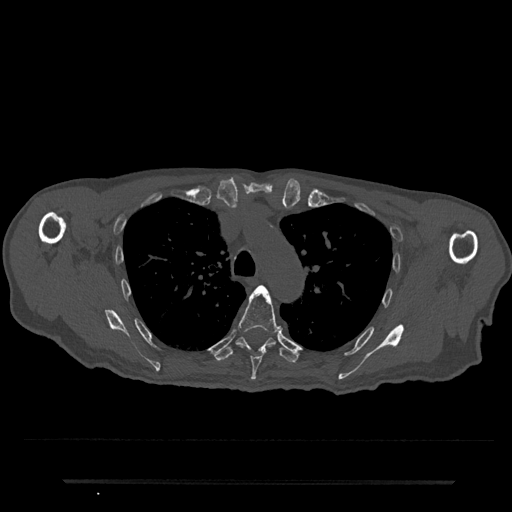
CT including the spine, one axial slice. Slice 563 of 797 in the series (ordered by position). Reconstruction kernel Br40s/3. Bone window (W 1800 / L 400 HU). 512 × 512 image matrix, field of view 427 × 427 mm. Male patient, age 74 years. From the clinical record (not read from this slice): primary cancer: prostate.
Structures marked on this image (semi-automatic segmentation, software-assisted and operator-edited):
- T5 vertebra: bounding box [x1, y1, x2, y2] px = [237, 285, 282, 381]
- T6 vertebra: [214, 337, 298, 364]